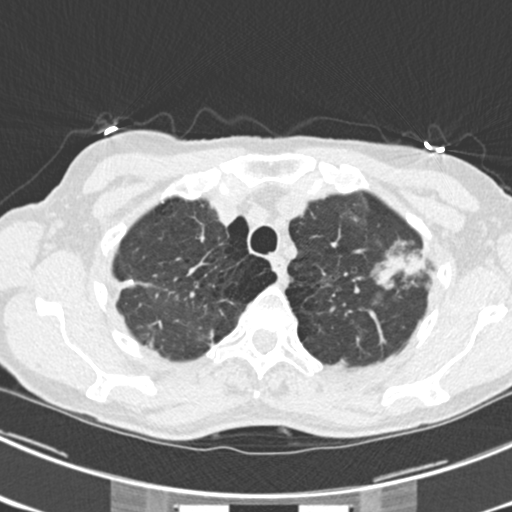
Low-dose screening chest CT, one axial slice. Slice 183 of 225 in the series (ordered by position). Lung window (W 1500 / L -600 HU). 512 × 512 image matrix.
Annotated regions visible in this slice (expert manual segmentation):
- lesion 1 (tumor, upper lobe of left lung): bounding box (x1, y1, x2, y2) in pixels: (377, 253, 425, 288)